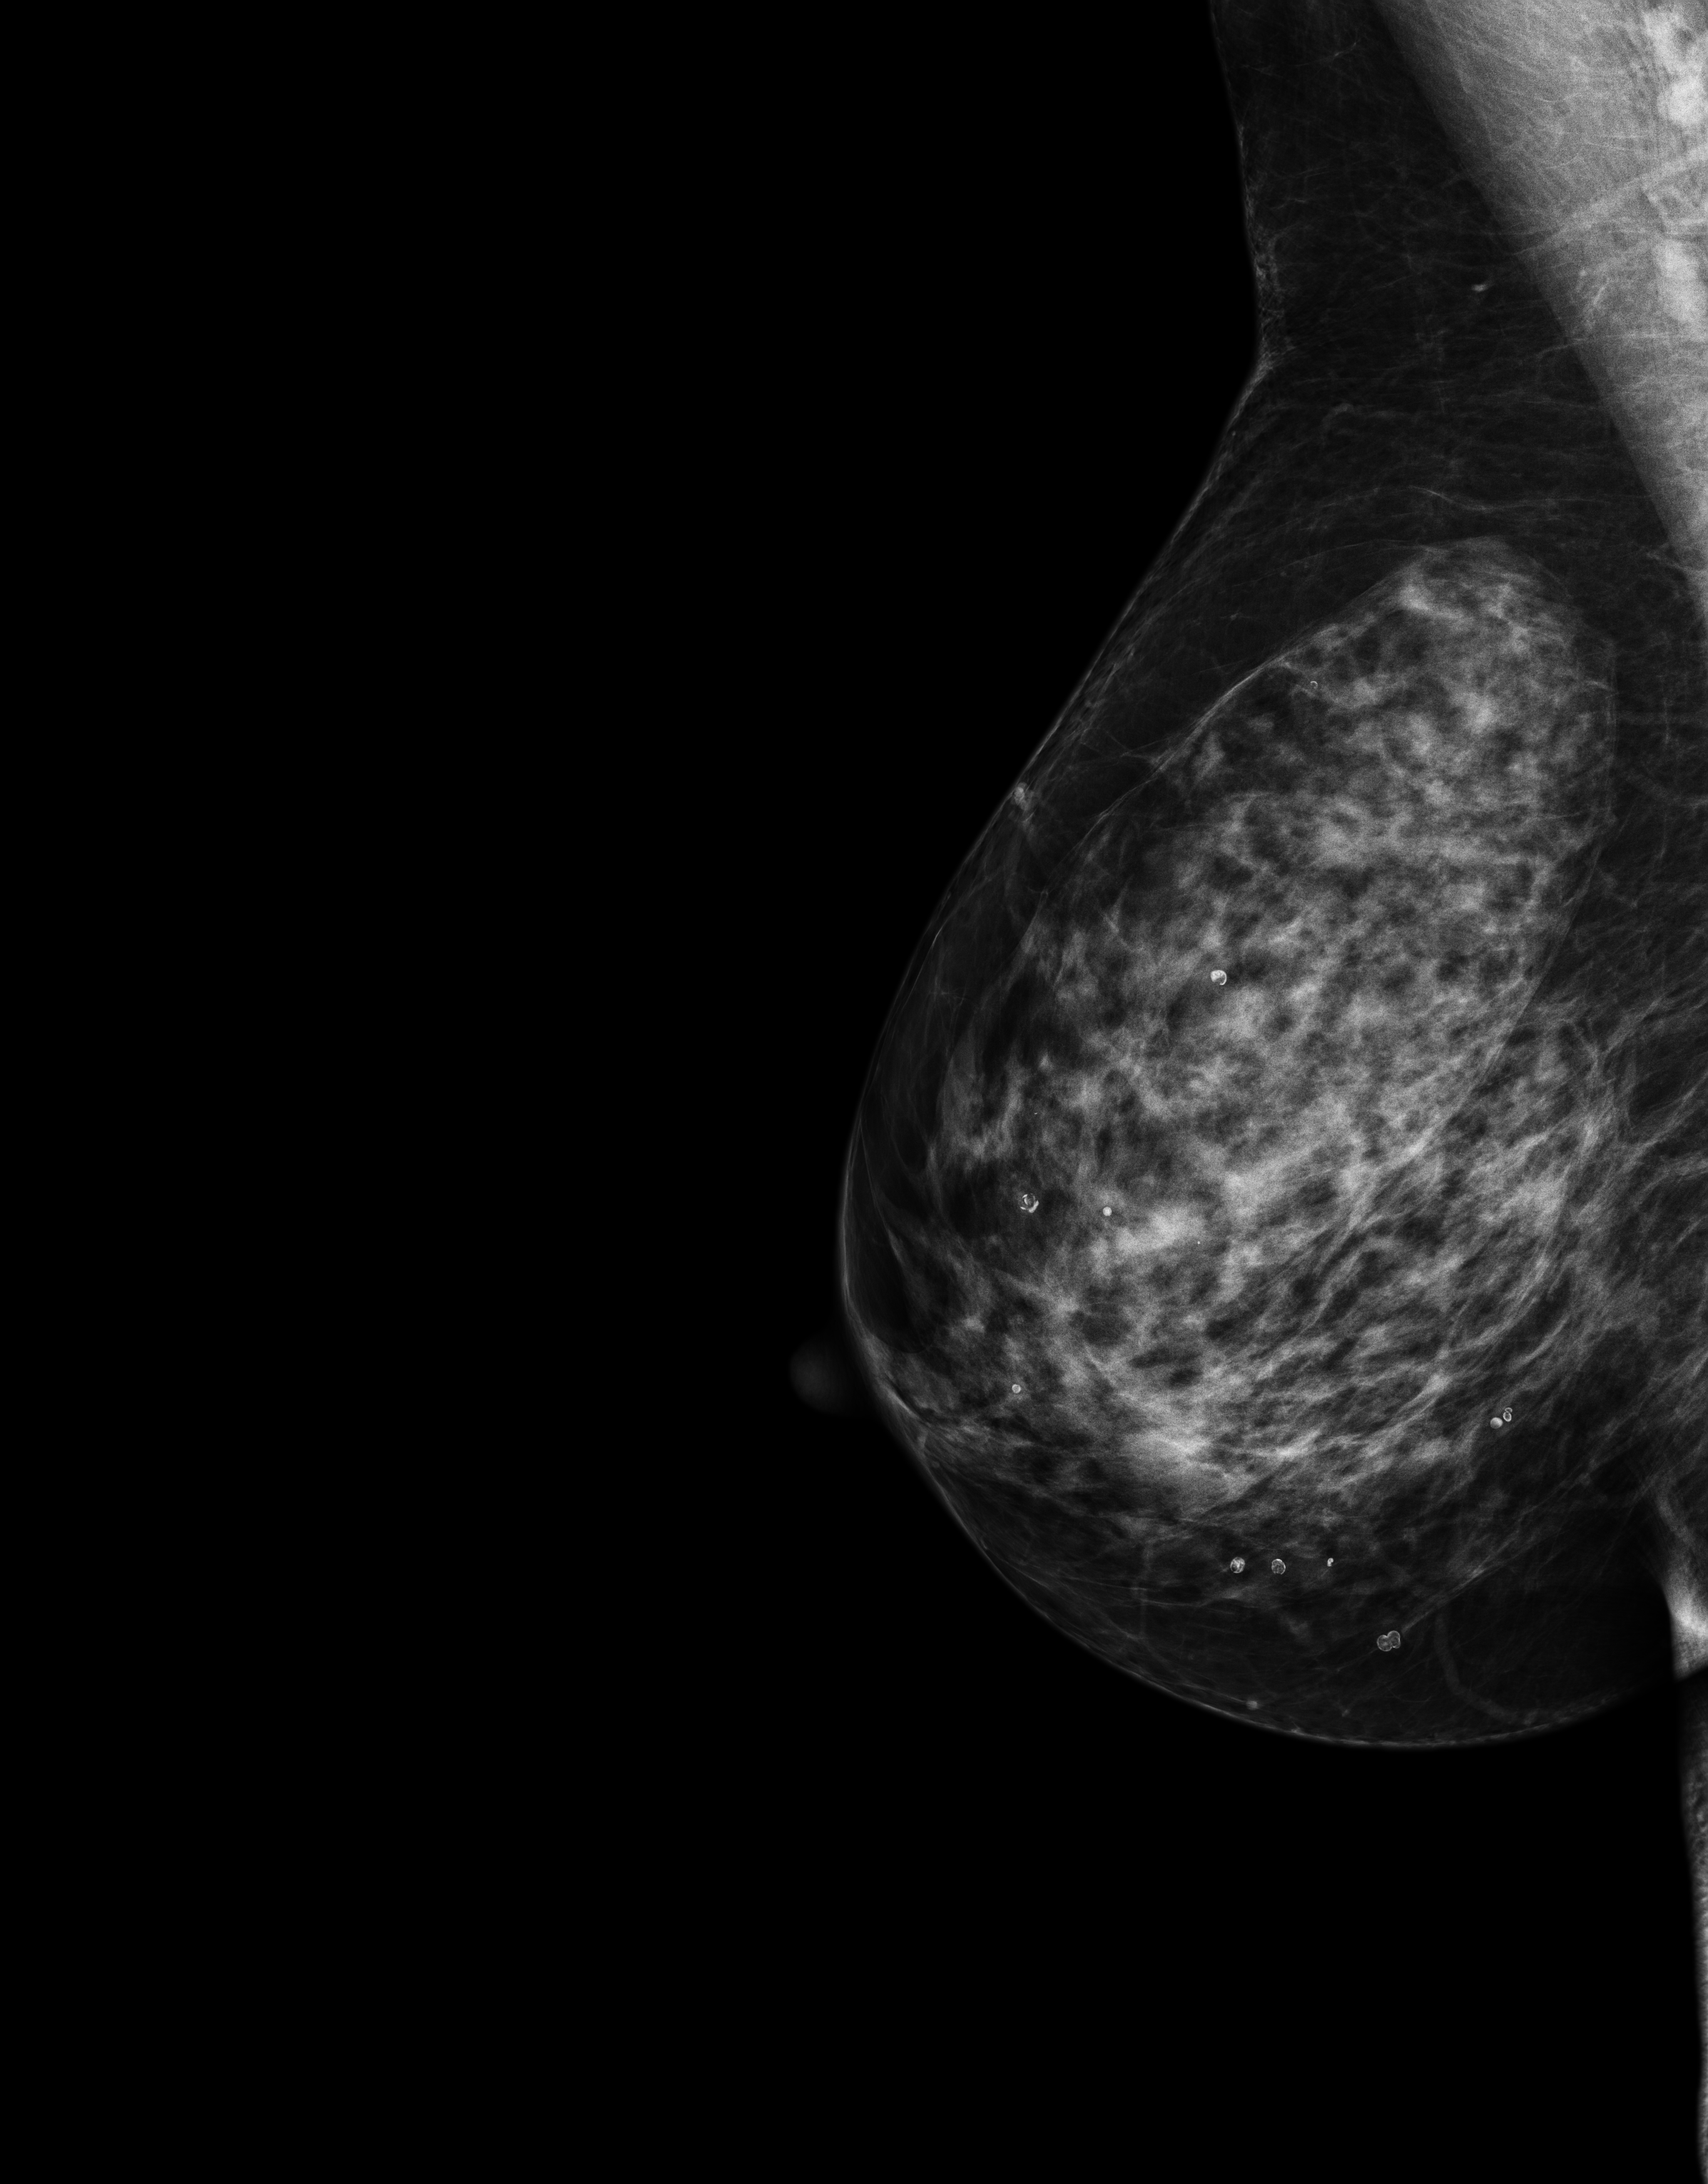
Digital mammogram (FFDM), right breast, mediolateral oblique (MLO) view, annual screening mammography examination, compressed breast thickness 70 mm, system: Senographe Essential ADS_56.21.3. Female patient, age 66 years.
- BI-RADS breast density category at the screening exam (both breasts, scale 1–4): 3
- final BI-RADS assessment for this screening round (tomosynthesis exam, both breasts): category 1
- recall: no recall after this screen